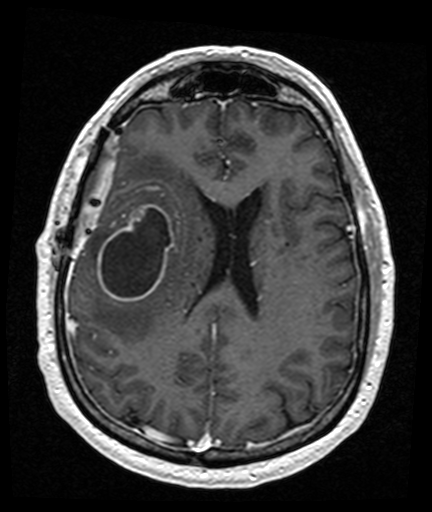
Brain MRI from a brain-tumour surgery series, one axial slice. Position 64 of 176 along the scan axis. T1-weighted post-contrast. 432 × 512 image matrix, field of view 194 × 230 mm. Case-level facts recorded for this patient, not image findings: histopathology: Glioblastoma; WHO grade: 4; IDH mutation: no.
Annotated regions visible in this slice (outlined manually by an expert reader):
- tumour: bounding box <98,204,174,302> (left, top, right, bottom; pixels)